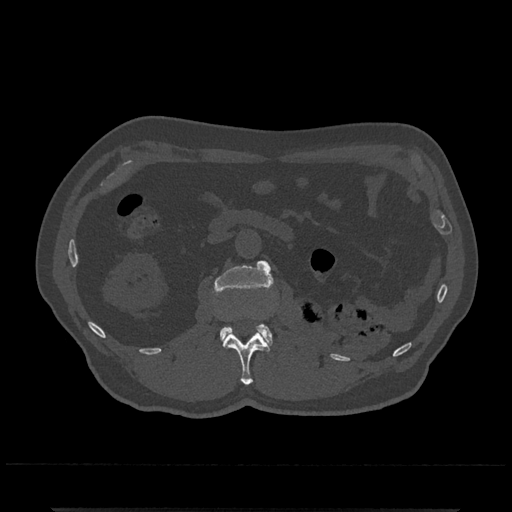
CT including the spine, one axial slice; position 330 of 797 along the scan axis; 120 kVp; bone window (W 1800 / L 400 HU); 512 × 512 image matrix, field of view 393 × 393 mm. Male patient, age 67 years. From the clinical record (not read from this slice): primary cancer: prostate.
Structures marked on this image (semi-automatically segmented with operator editing):
- L1 vertebra: bounding box [x1, y1, x2, y2] px = [223, 332, 269, 385]
- L2 vertebra: [212, 260, 273, 346]